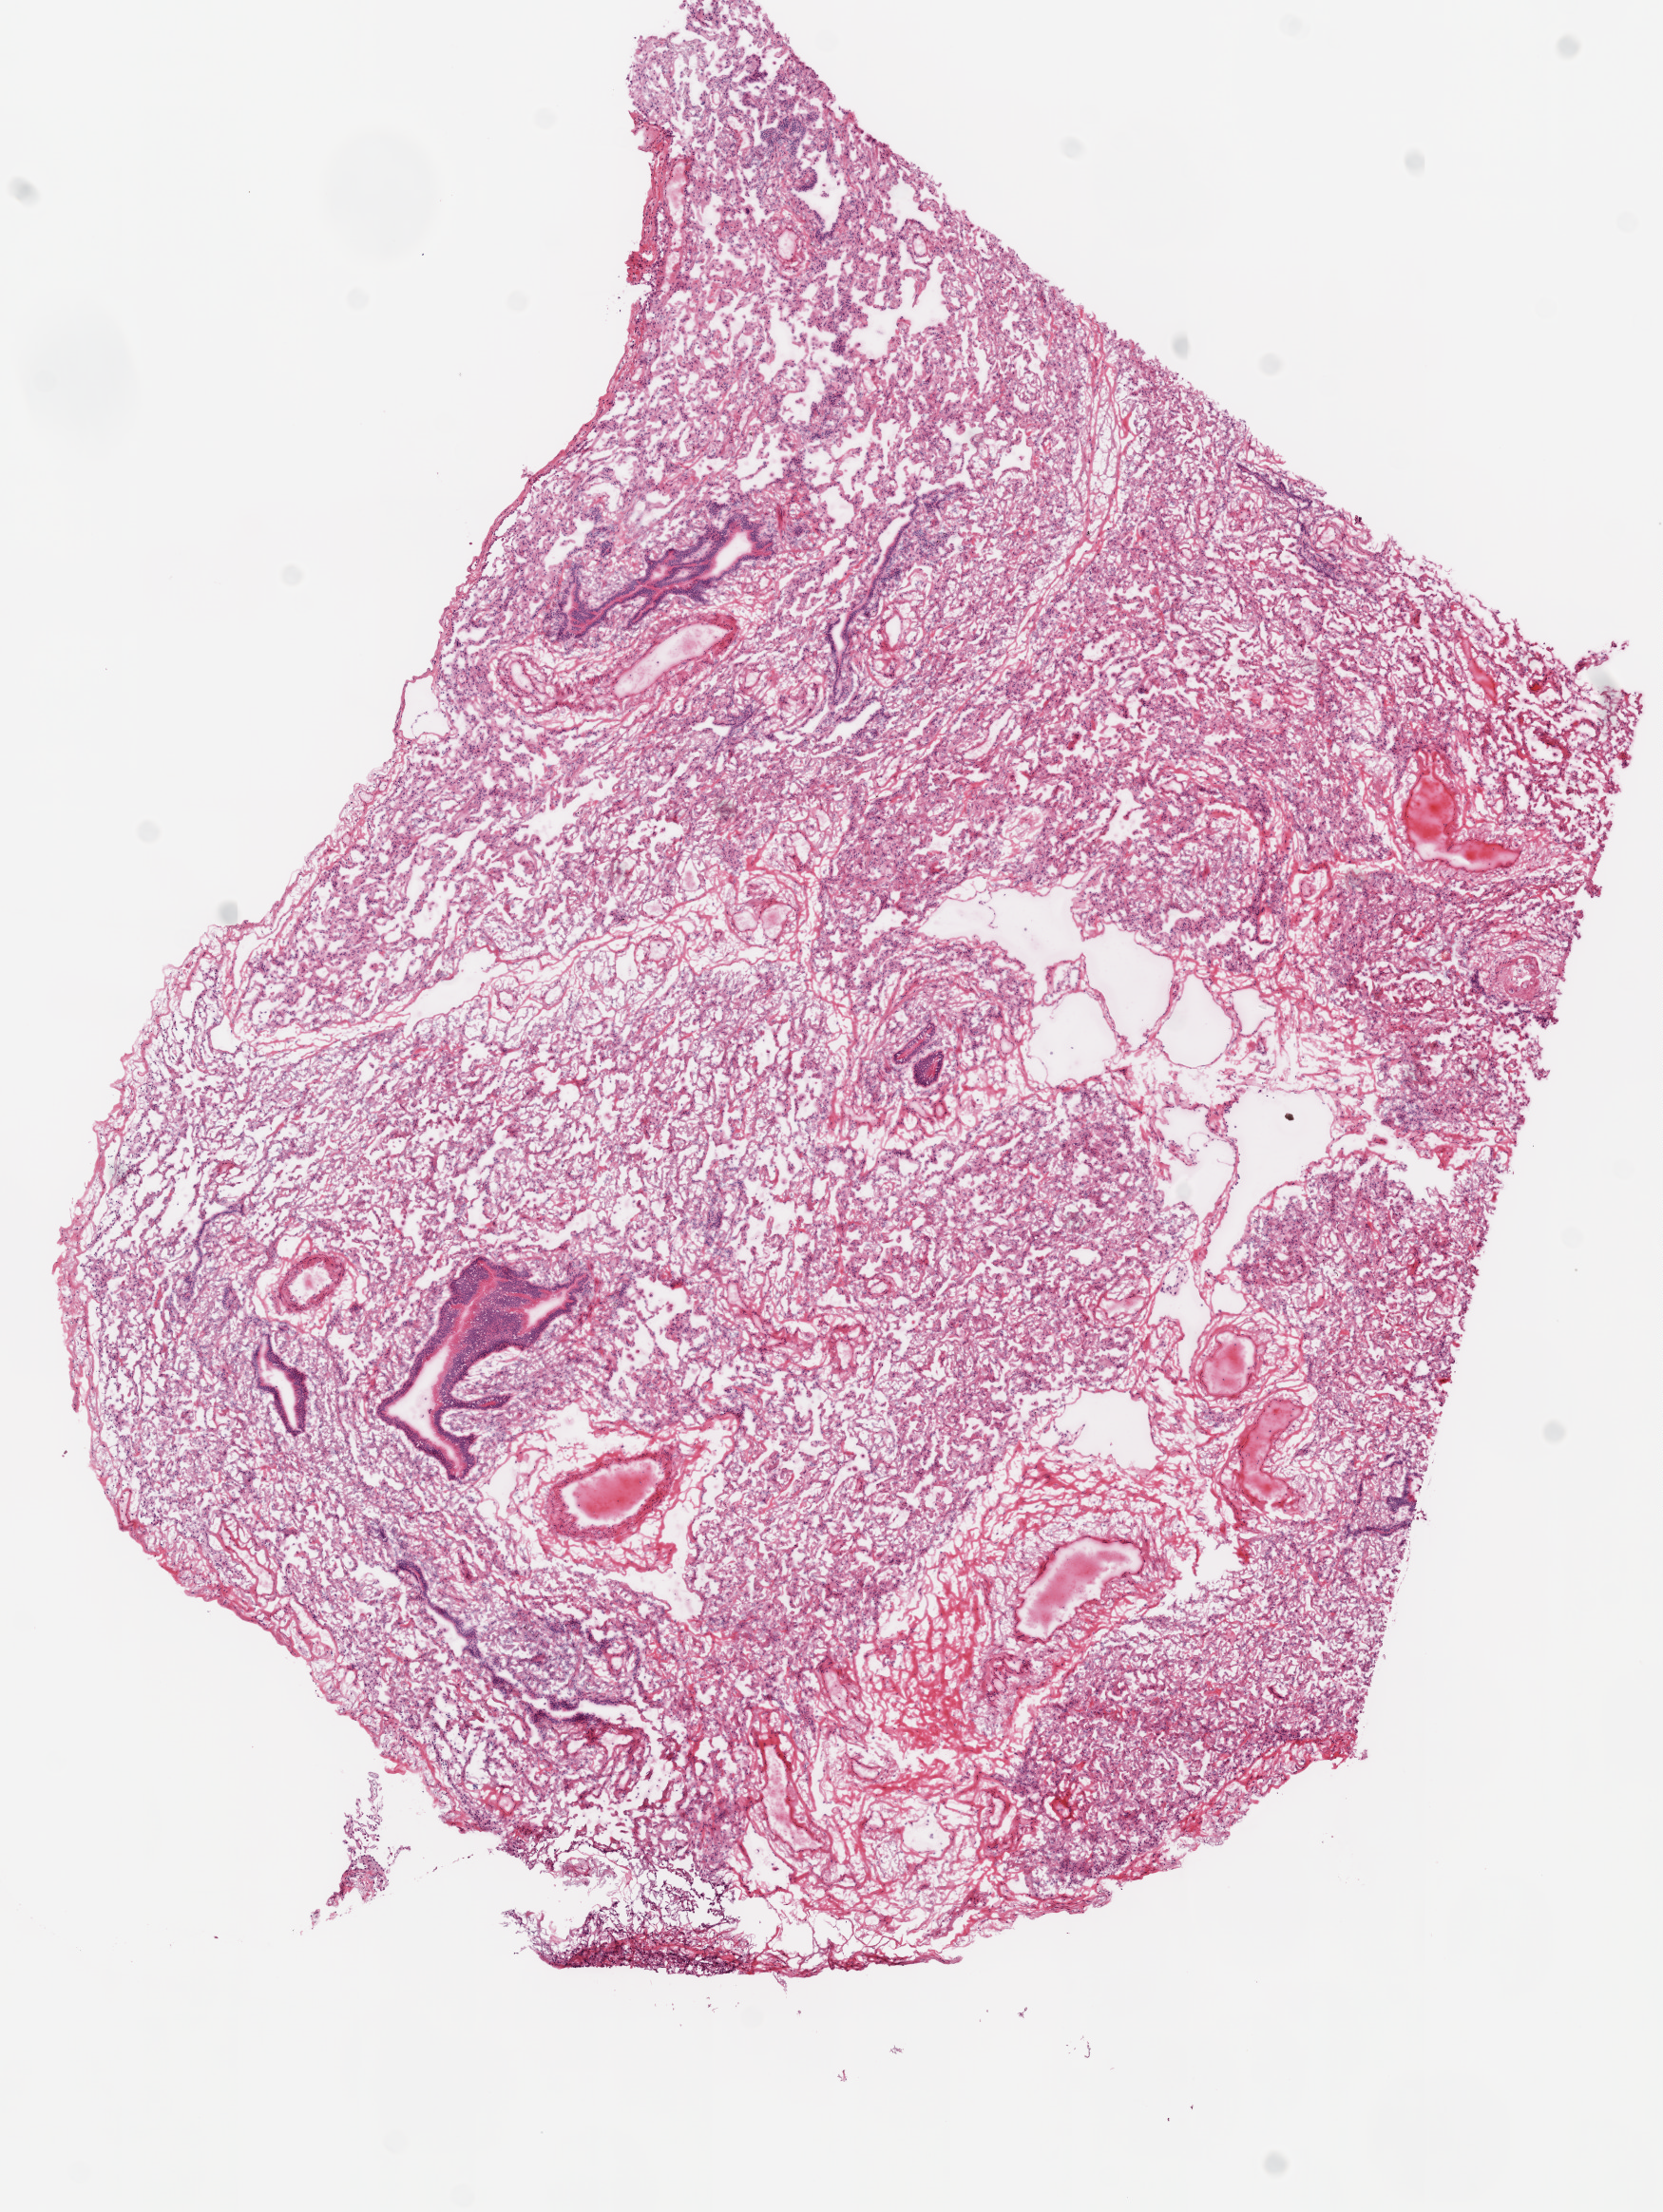
Hematoxylin and eosin (H&E) stained whole-slide image, a low-resolution overview of the entire scanned area, about 7.0 x 9.3 mm (slide scanned at 20x), frozen section from the top of the tissue portion, solid tissue normal (non-tumour tissue) sample from the lung. Patient: female, age at initial diagnosis 69 years.
This section: solid tissue normal (non-tumour) sample from the same patient. Patient diagnosis: Squamous cell carcinoma, NOS (upper lobe, lung).